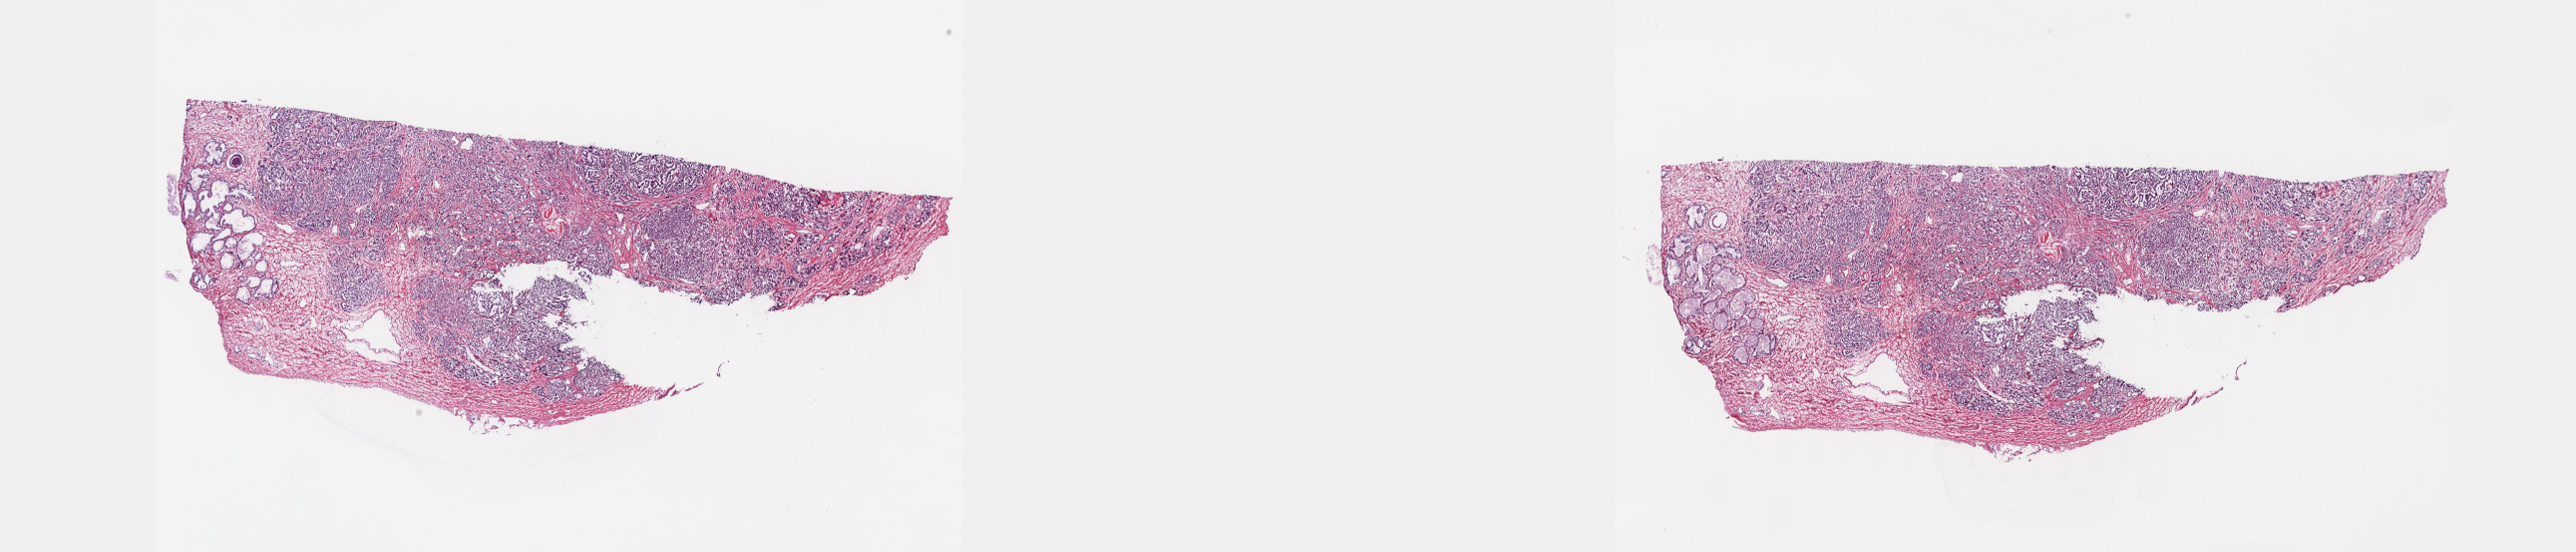
Hematoxylin and eosin (H&E) stained whole-slide image, whole scanned area (about 41.7 x 8.9 mm, from a 40x scan) shown as a low-resolution overview; frozen section from the top of the tissue portion; prostate, primary tumour sample. Patient: male, age at initial diagnosis 64 years. Composition of this section per pathologist review: tumour cells 60%, tumour nuclei 70%.
Histologic diagnosis: Adenocarcinoma, NOS (prostate gland).